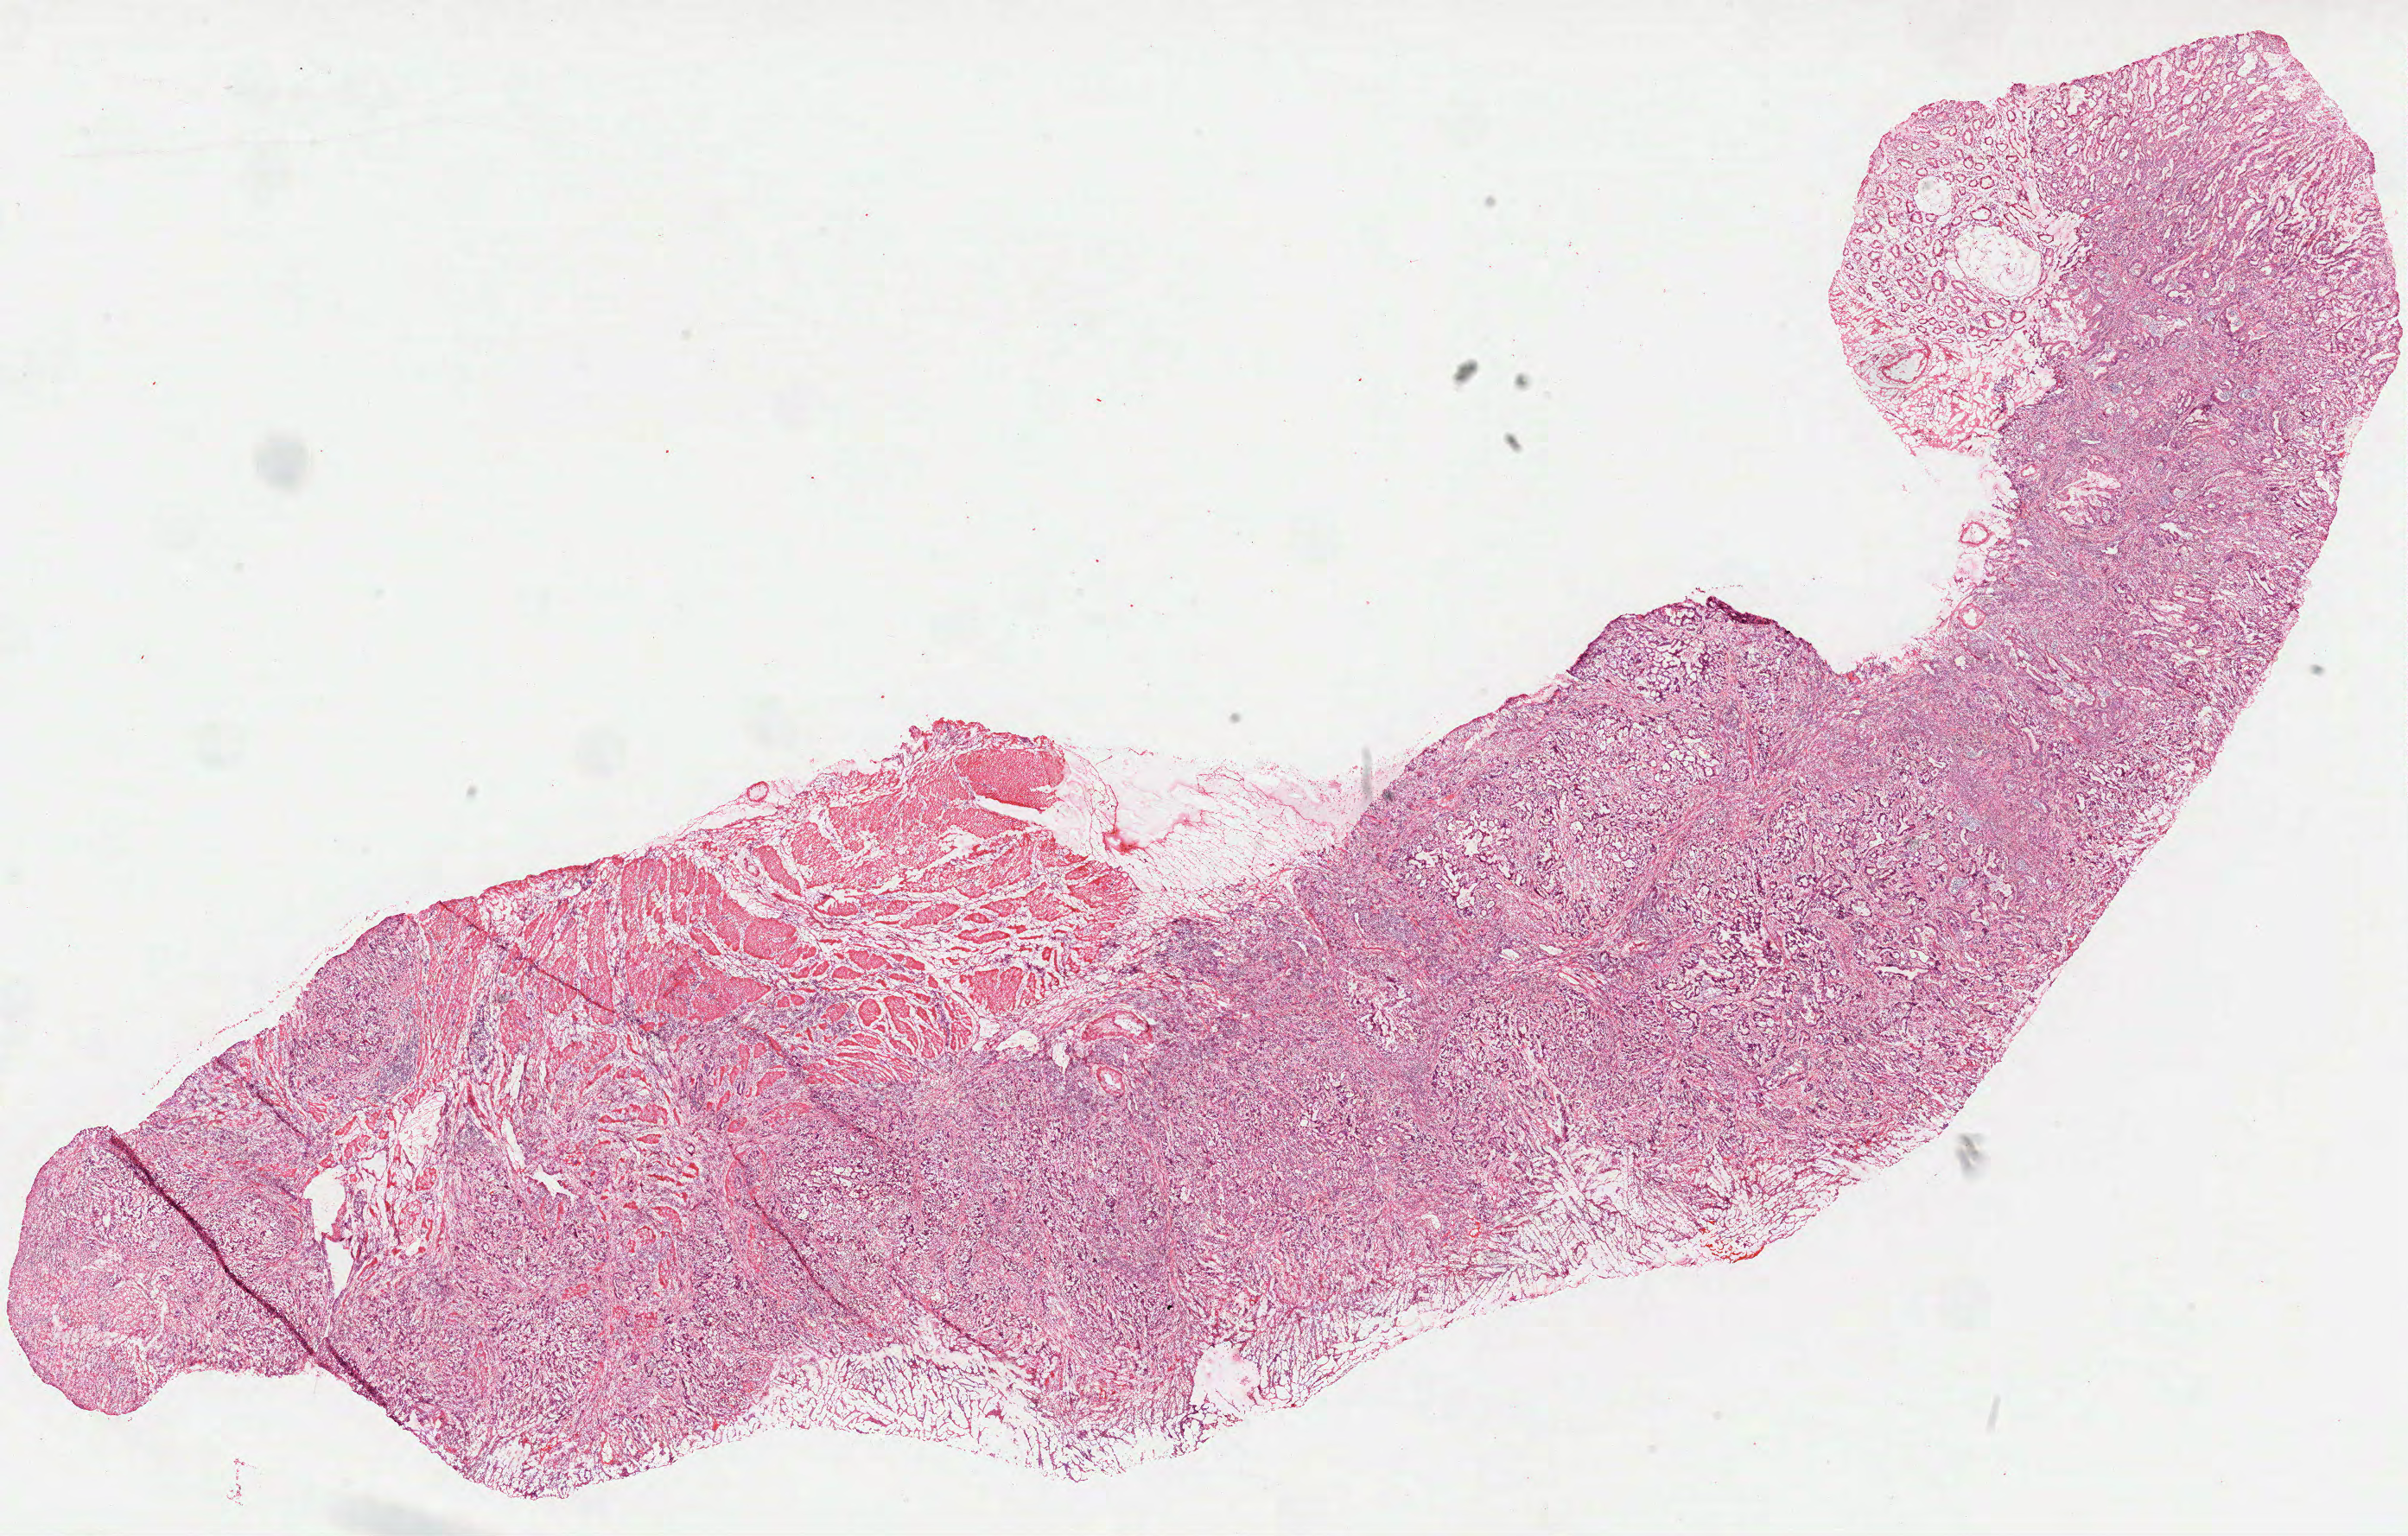
Whole-slide histology image, H&E — whole scanned area (about 22.5 x 14.3 mm, slide scanned at 40x) shown as a low-resolution overview. Frozen section from the top of the tissue portion. Stomach, primary tumour sample. Male, age 79 years at initial diagnosis. Histologic grade: G3 (poorly differentiated). Composition of this section per pathologist review: tumour cells 75%, tumour nuclei 75%, normal cells 5%, stromal cells 20%, necrosis 0%.
Histologic diagnosis: Adenocarcinoma, NOS (gastric antrum). AJCC pathologic stage: IIIC (7th edition).